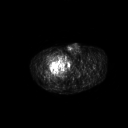
FDG PET of an extremity soft-tissue mass (from a PET/CT study), one axial slice; position 284 of 311 along the scan axis; 128 × 128 image matrix, field of view 700 × 700 mm. Male patient, age 50 years. From the clinical record (not read from this slice): histological type: undifferentiated - pleiomorphic; grade: high; site of the primary tumour: right thigh.
Annotated regions visible in this slice (expert contour drawn on MRI and transferred to this co-registered scan by the dataset authors):
- gross tumour volume including surrounding oedema: bounding box (x1, y1, x2, y2) in pixels: (51, 53, 65, 67)
- gross tumour volume (mass): (51, 54, 64, 67)